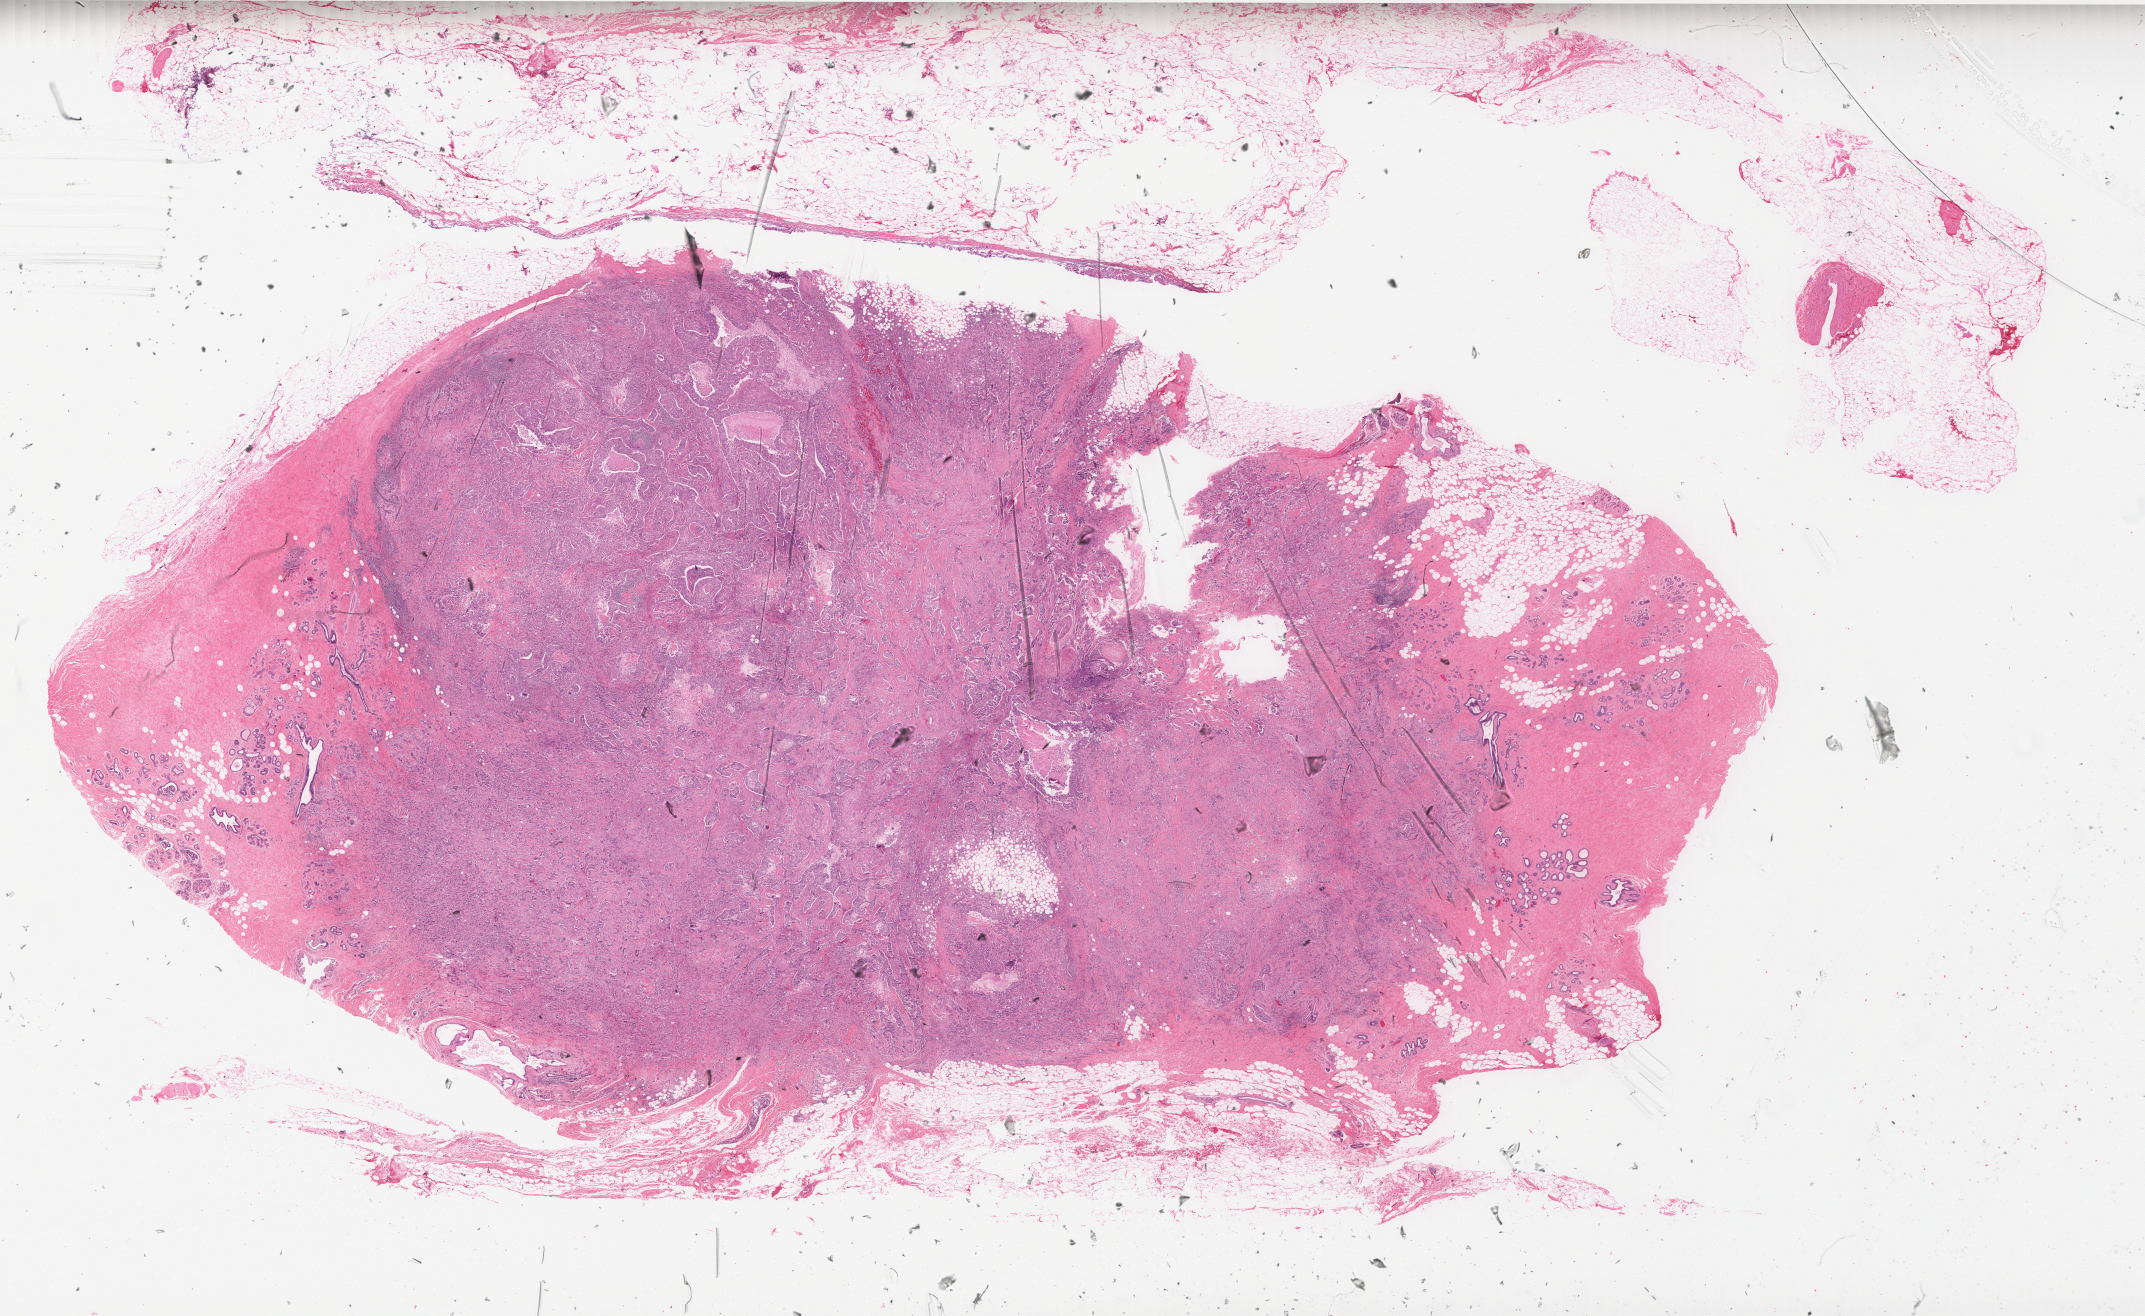
H&E whole-slide image, whole scanned area (about 34.4 x 21.1 mm, slide scanned at 40x) shown as a low-resolution overview; formalin-fixed paraffin-embedded (FFPE) diagnostic section; breast, primary tumour sample. Female, age 38 years at initial diagnosis.
* lymph nodes positive (case pathology): 0 of 15 examined
* diagnosis: Infiltrating duct carcinoma, NOS
* TNM: T2 N0 (i-) M0
* laterality: left
* AJCC pathologic stage: IIA